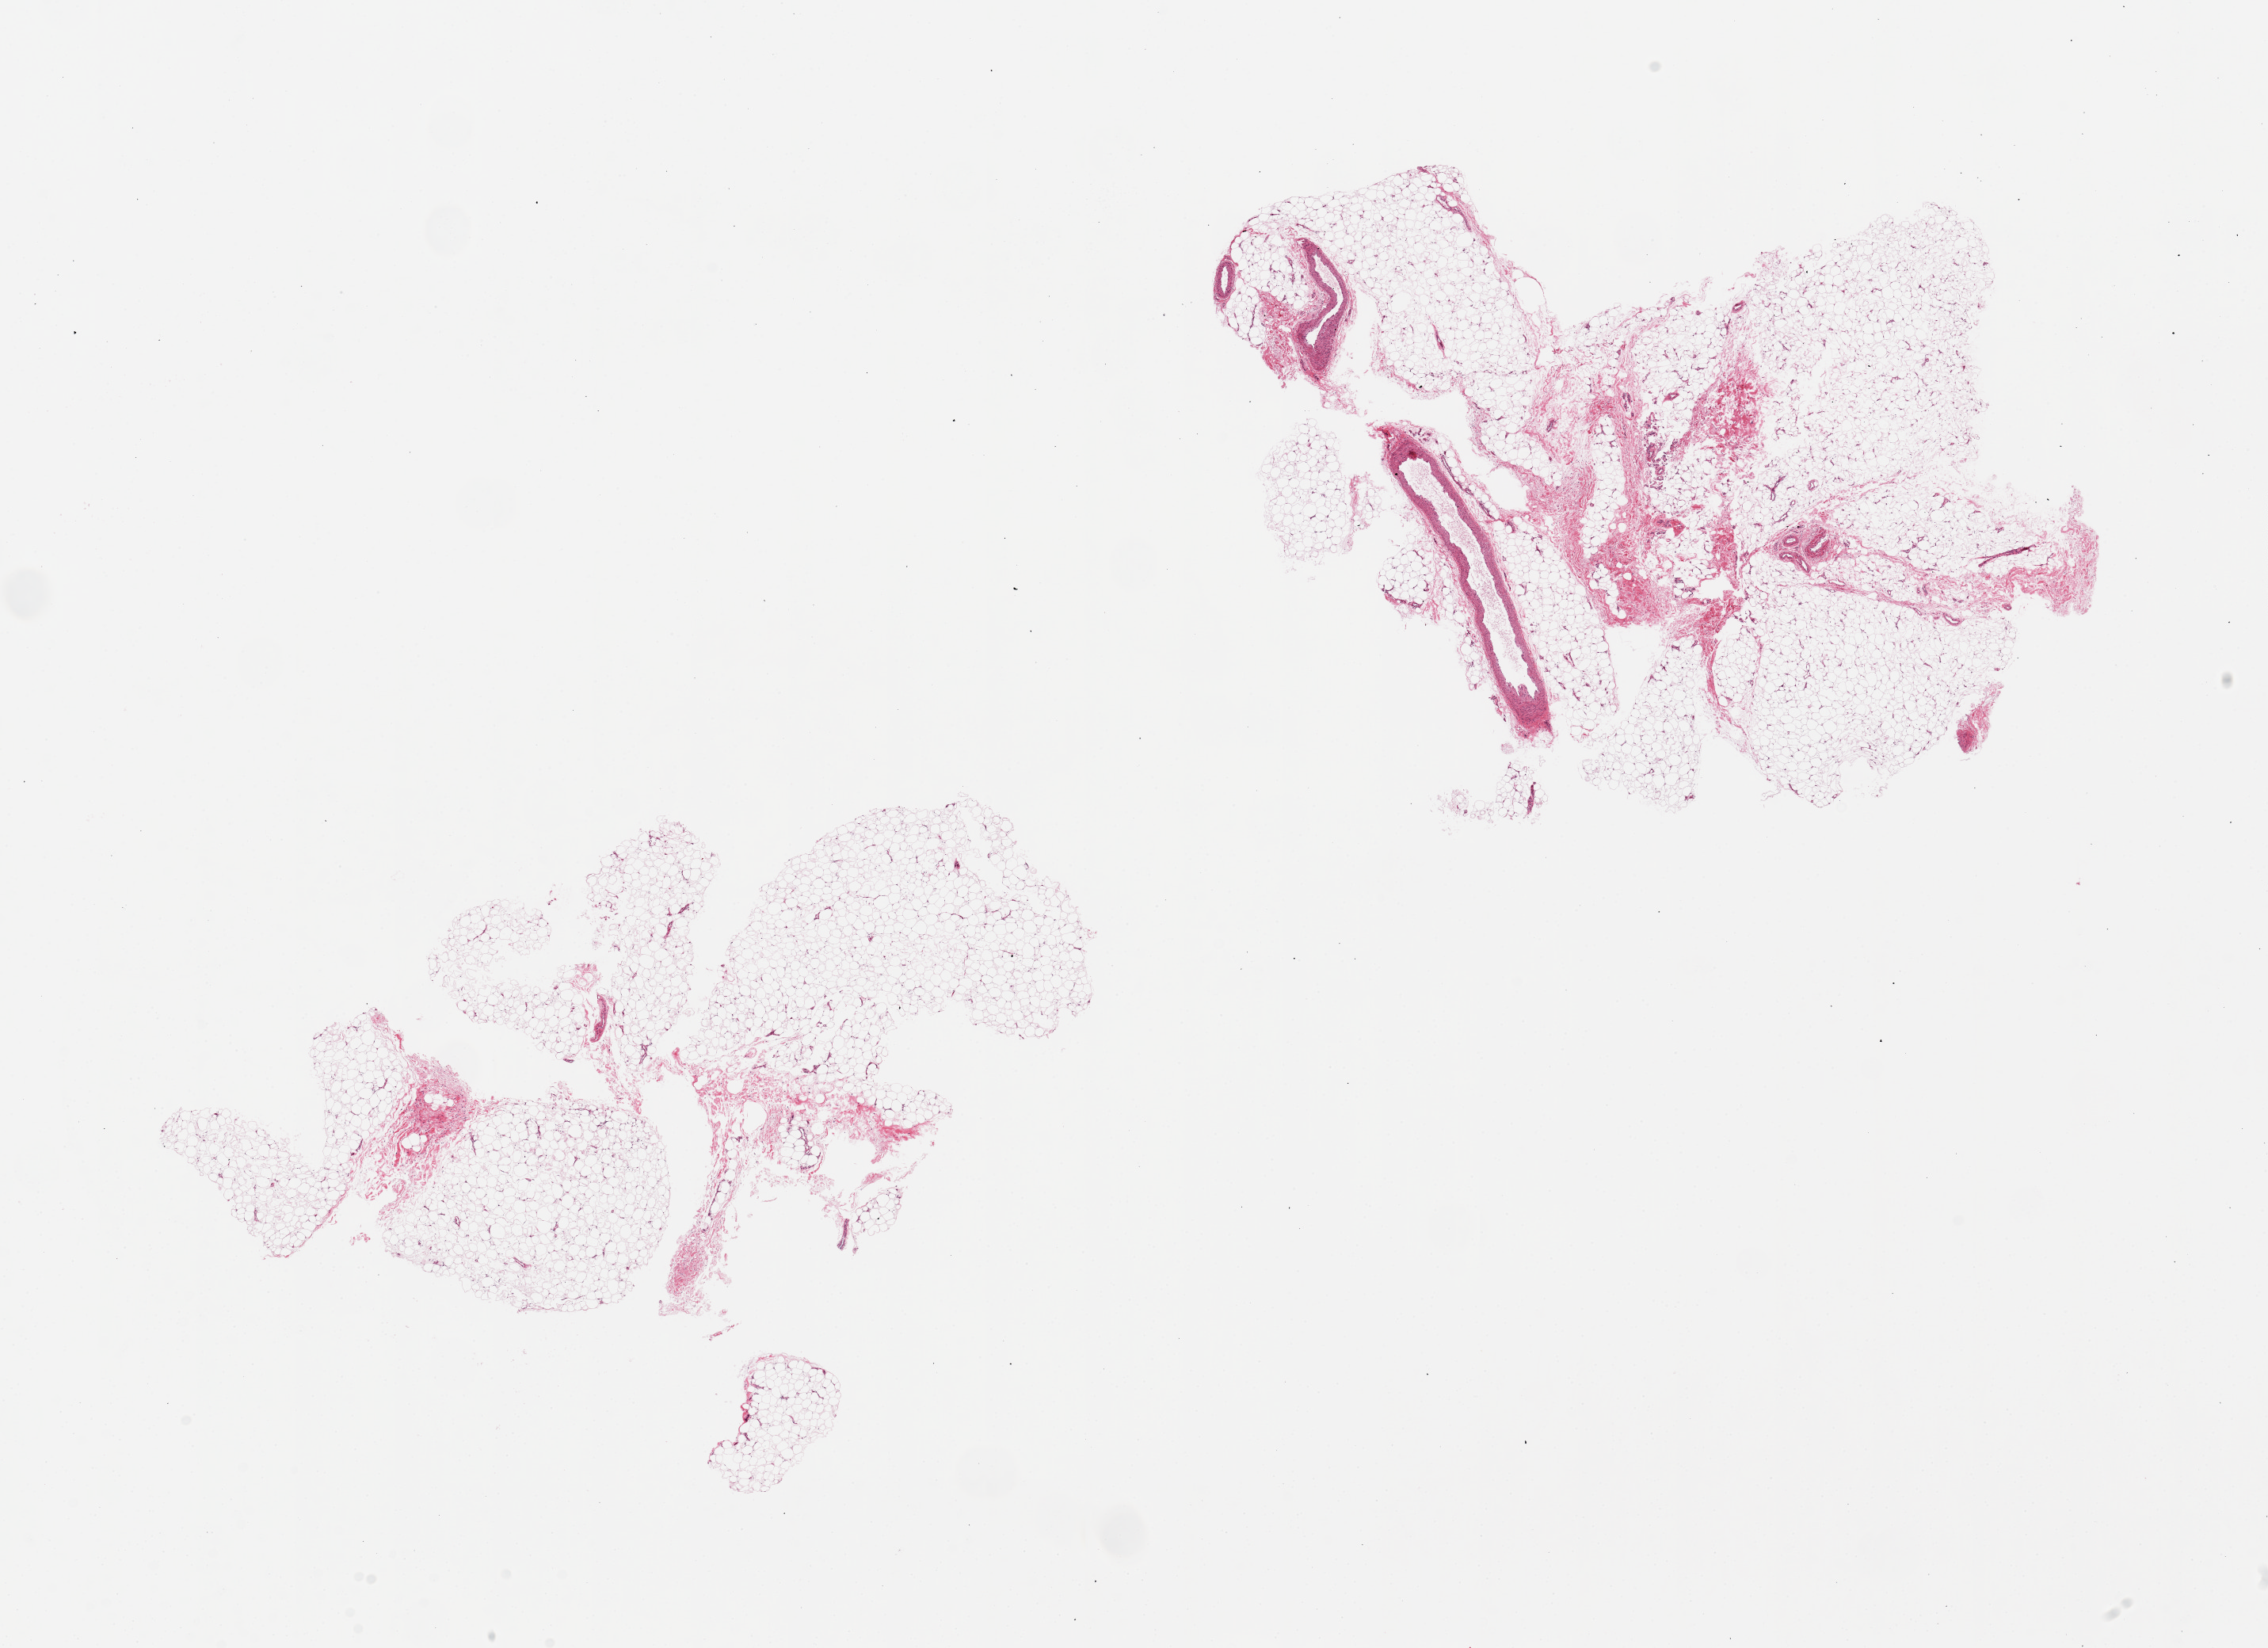
Whole-slide image, haematoxylin and eosin stain, brightfield, low-resolution overview of the scanned area, about 22.6 x 16.4 mm (from a 20x scan); PAXgene-fixed, paraffin-embedded tissue; sampled site (target tissue): adipose tissue; donor tissue sample.
• pathologist's review note for this sample: 2 pieces, fibroadipose tissue